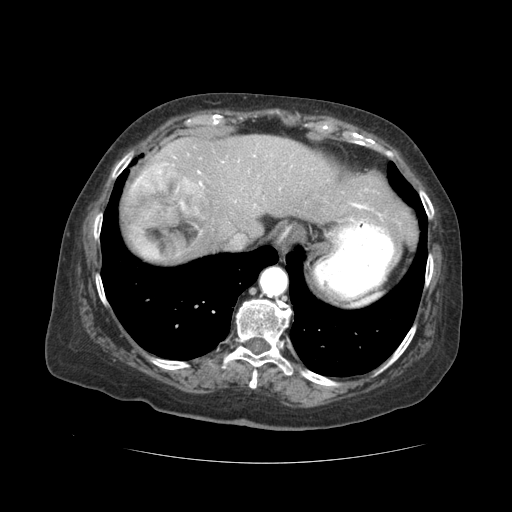
Contrast-enhanced abdominal CT (liver protocol), one axial slice. Position 39 of 59 along the scan axis. Reconstruction kernel STANDARD. Soft-tissue window (W 400 / L 40 HU). 2.5 mm slice thickness. 512 × 512 image matrix, field of view 380 × 380 mm. Case-level facts recorded for this patient, not image findings: diagnosis: hepatocellular carcinoma (patient treated with transarterial chemoembolisation; whether this scan precedes or follows treatment is not stated here); TNM stage (as recorded): Stage-I; Child-Pugh class: A; tumour nodularity: uninodular.
Annotated regions visible in this slice (semi-automatically segmented with operator editing):
- liver parenchyma outside the tumour (the mass and vessels are separate outlines, so this box may not span the whole liver): bounding box <124,134,414,262> (left, top, right, bottom; pixels)
- mass: <125,163,209,260>
- liver vessels: <174,157,381,216>